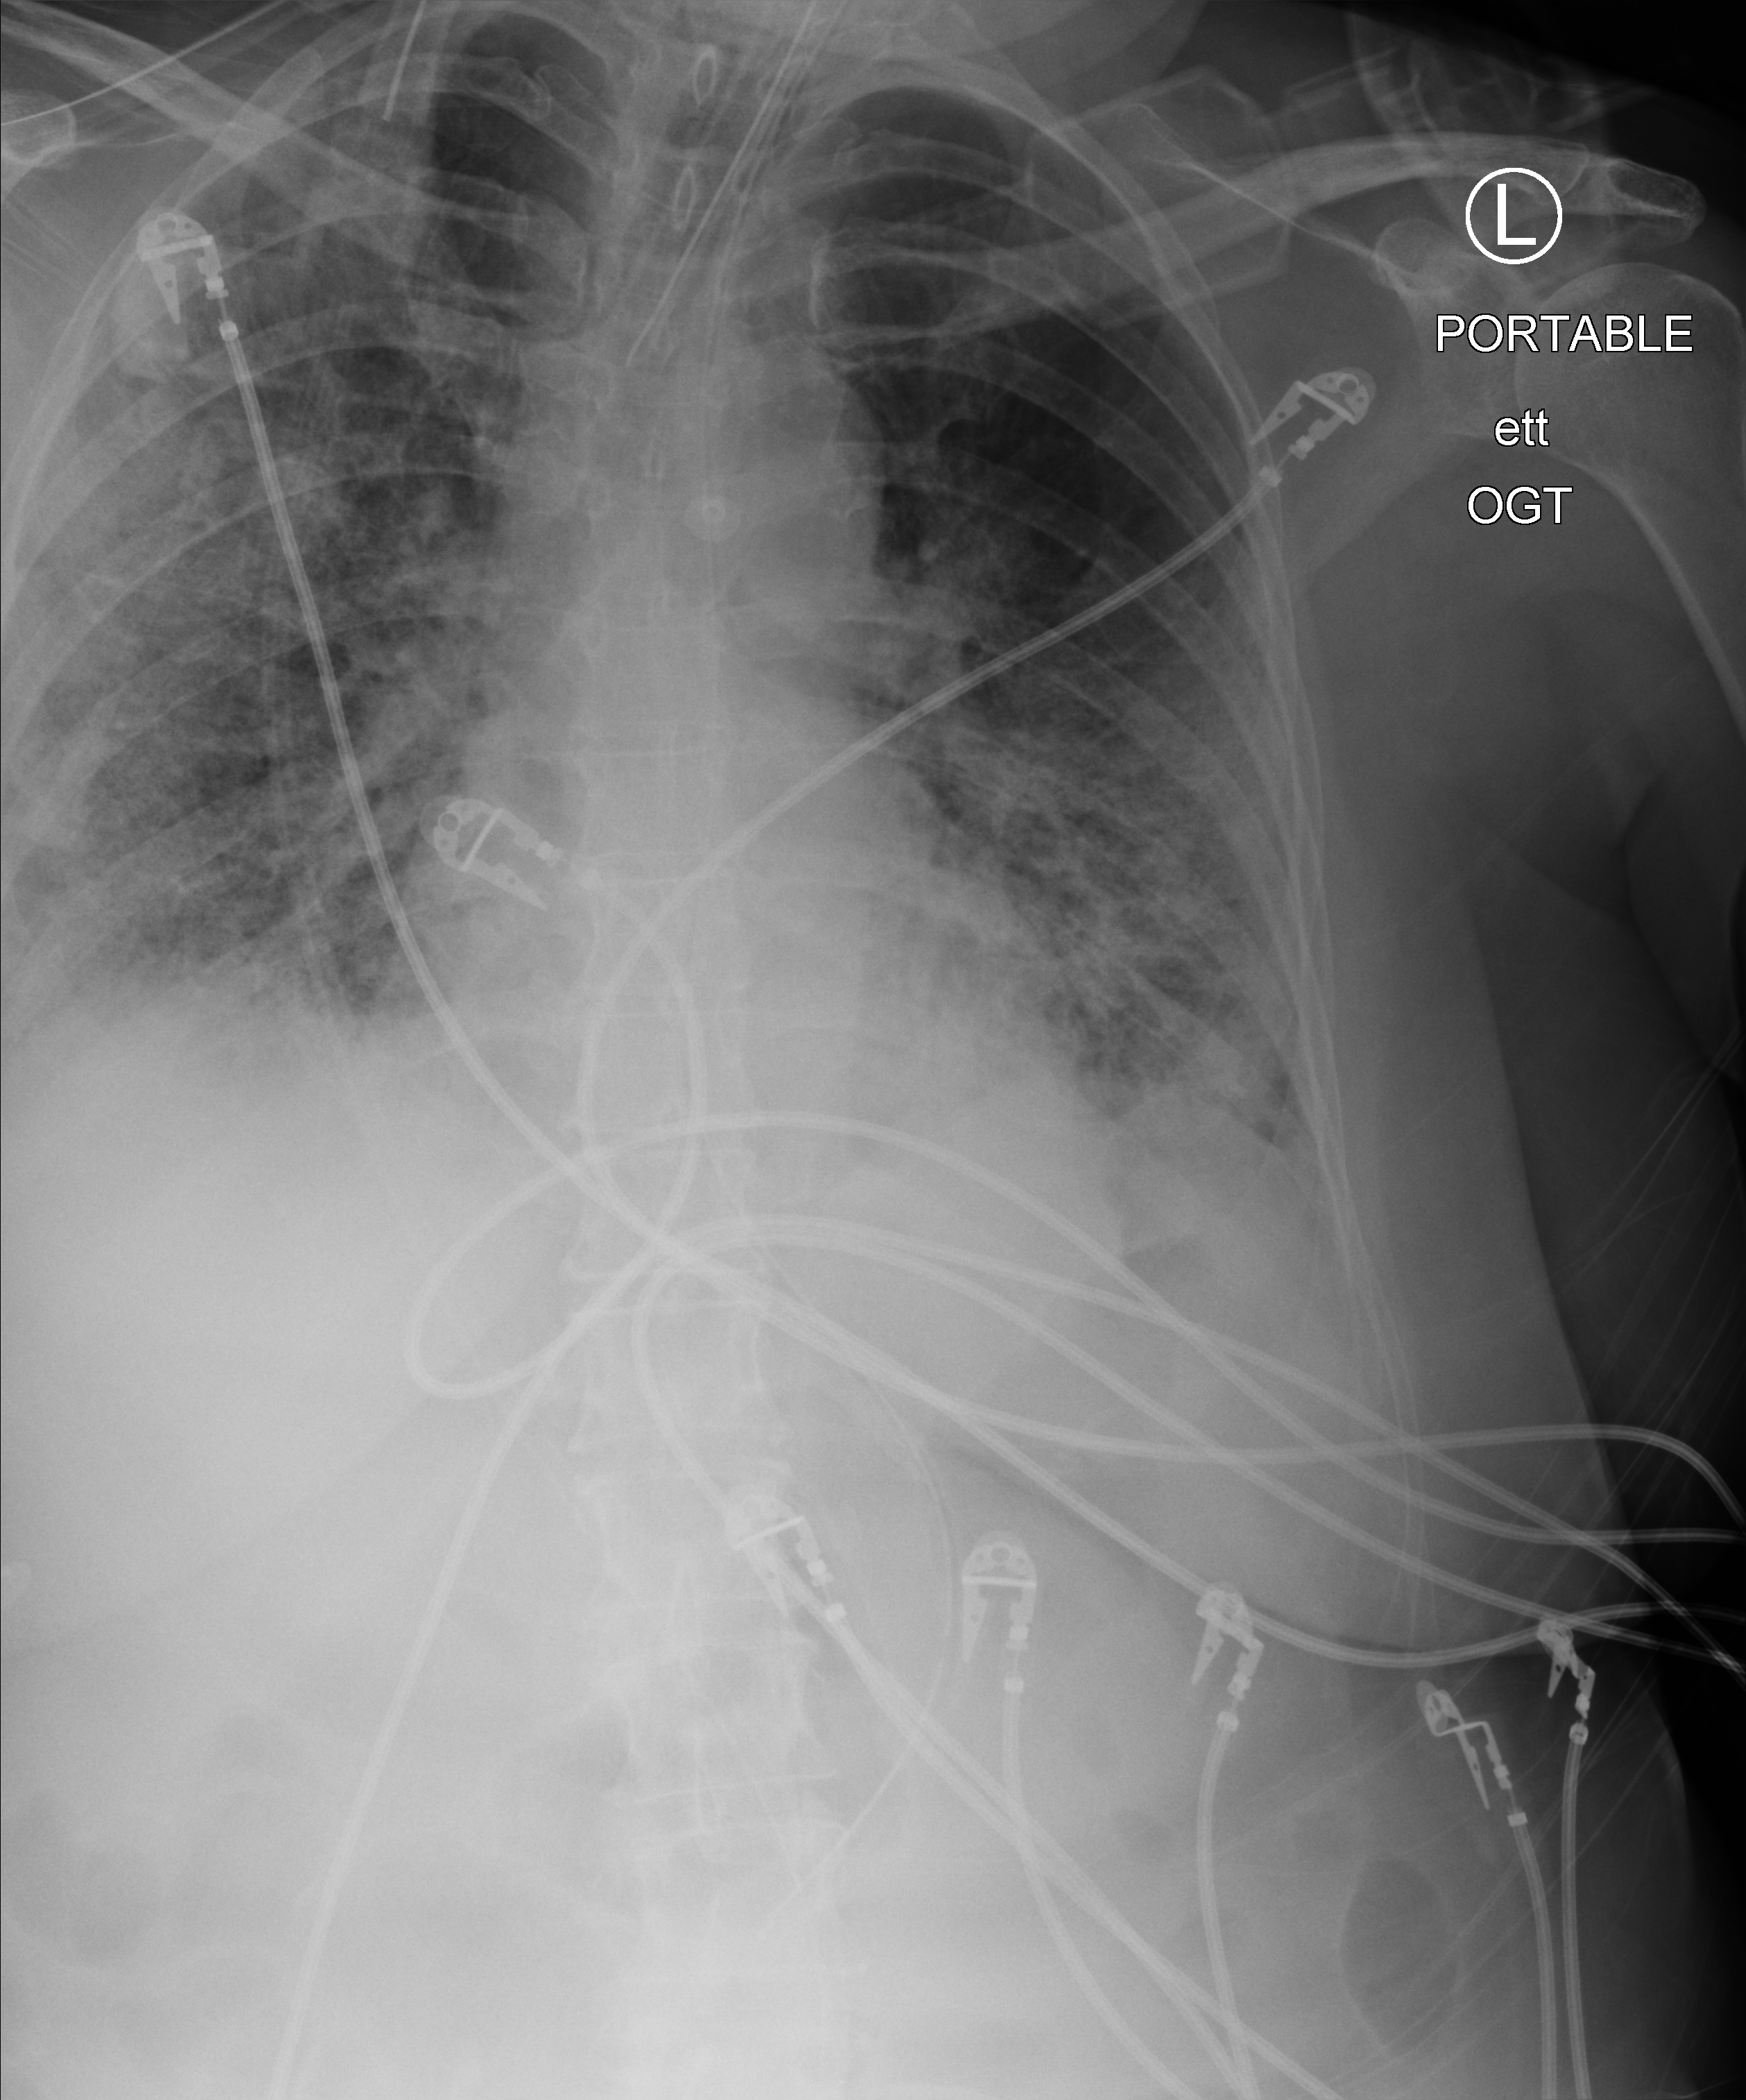
Bedside chest radiograph (computed radiography); anteroposterior (AP) projection. Female patient hospitalised with COVID-19, age 60–74 years.
Hospital-stay facts (about this admission, not read from this image; timing relative to this image not recorded): mechanically ventilated during this hospital stay: yes.